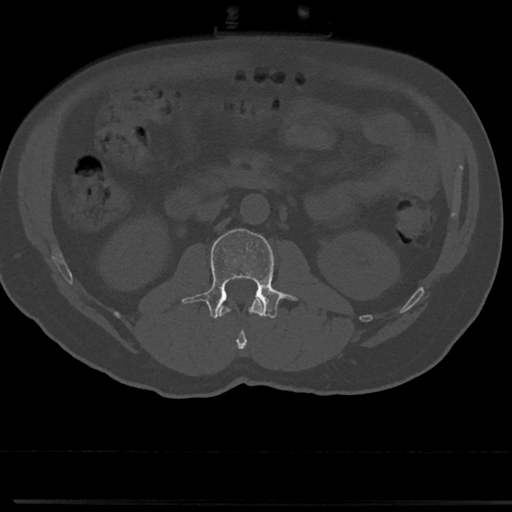
CT including the spine, one axial slice. Slice 30 of 817 in the series (ordered by position). 120 kVp. Bone window (W 1800 / L 400 HU). 0.5 mm slice thickness. 512 × 512 image matrix. Male patient, age 61 years. From the clinical record (not read from this slice): primary cancer: prostate.
Structures marked on this image (semi-automatic segmentation, software-assisted and operator-edited):
- L1 vertebra: bounding box [x1, y1, x2, y2] px = [219, 298, 263, 351]
- L2 vertebra: [191, 228, 296, 319]